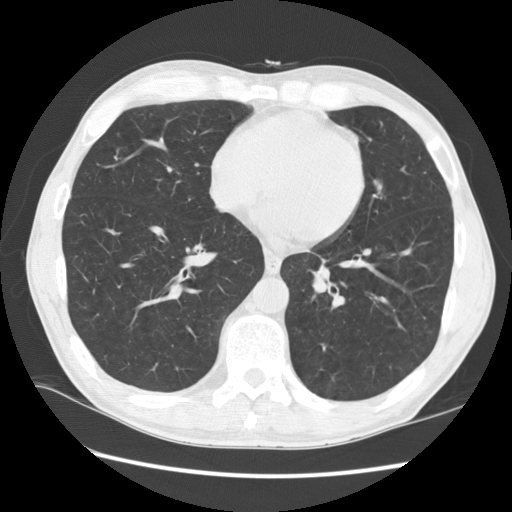
Chest CT (low-dose screening protocol), one axial image; baseline screening round; lung window (W 1500 / L -600 HU); 2.5 mm slice thickness; standard (soft-tissue) reconstruction kernel (STANDARD); 120 kVp; slice 93 of 141 in the series. Male participant, aged 57 years at enrolment. Current smoker at enrolment.
Lesion marked by an expert reader, bounding box <267,249,344,315> (left, top, right, bottom; pixels). The screening reader recorded 2 non-calcified nodules or masses ≥4 mm on this exam (left lower lobe, lingula); which of them this box marks is not recorded. Official screen result: positive, change unspecified: nodule(s) >= 4 mm or enlarging nodule(s), mass(es), or other non-specific abnormalities suspicious for lung cancer. Participant outcome: lung cancer diagnosed 95 days after this screen — squamous cell carcinoma, NOS, left lower lobe, moderately differentiated (G2), stage IB (AJCC 6th edition), 35 mm at pathology.